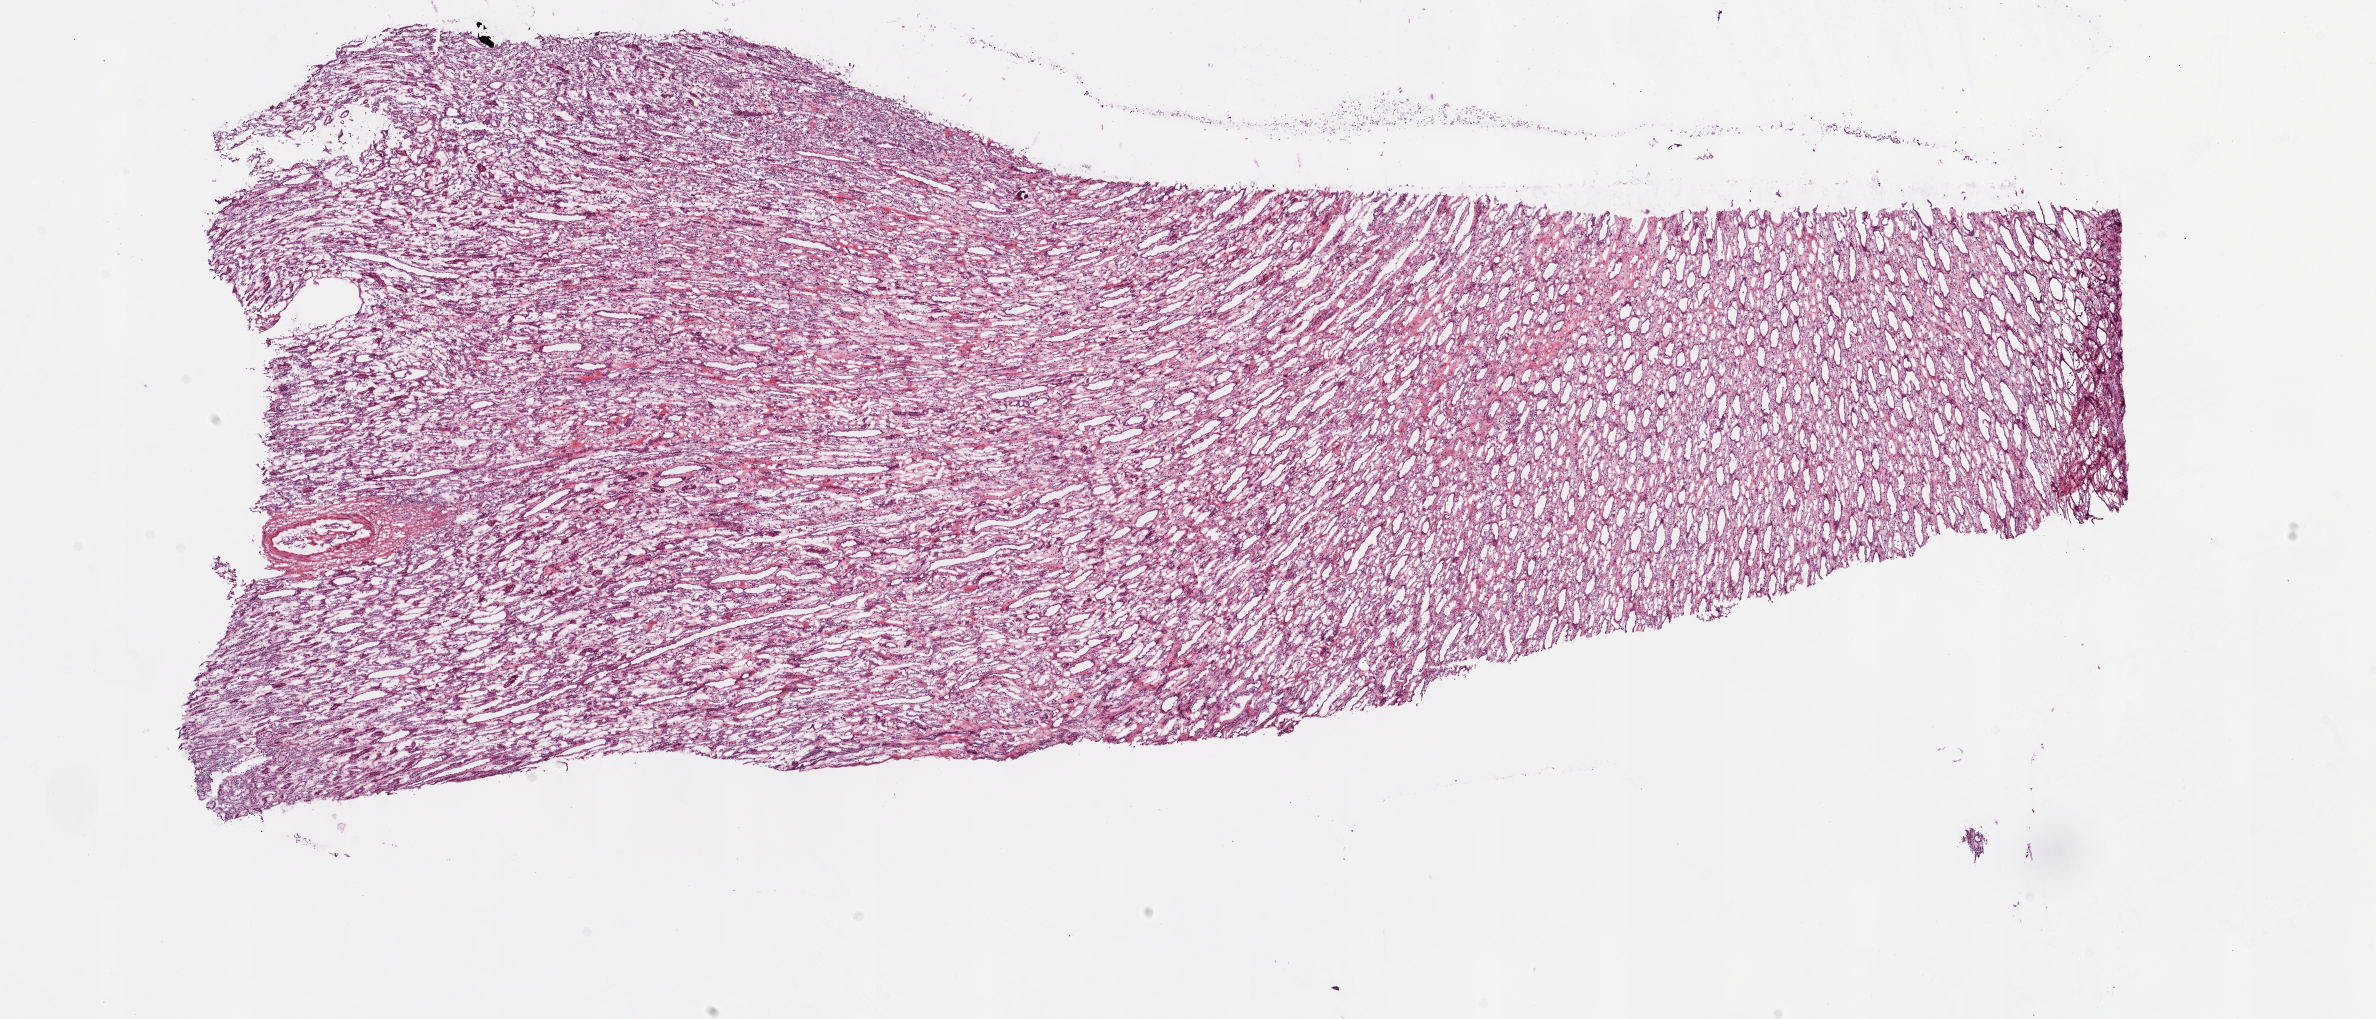
Whole-slide histology image, Hematoxylin and eosin (H&E) stained, whole scanned area (about 18.8 x 8.1 mm) shown as a low-resolution overview, frozen section from the bottom of the tissue portion, kidney, solid tissue normal (non-tumour tissue) sample. Male patient; age at initial diagnosis 46 years.
• this section: solid tissue normal sample (biorepository sample class)
• patient diagnosis: Clear cell adenocarcinoma, NOS